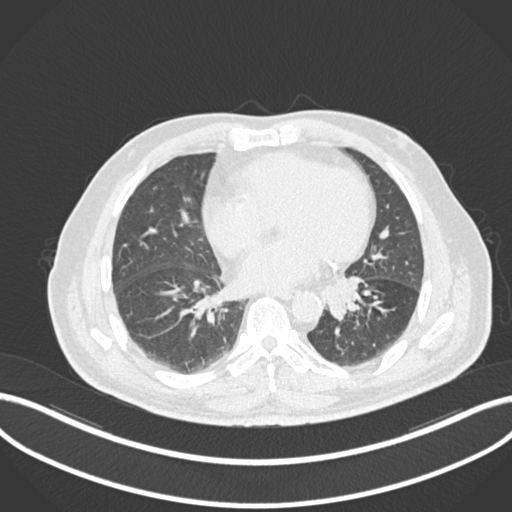
Chest CT, one axial slice; position 46 of 161 along the scan axis; lung window (W 1500 / L -600 HU); 512 × 512 image matrix, field of view 400 × 400 mm. Male patient, age 71 years. Case-level facts recorded for this patient, not image findings: clinical TNM (as recorded): T1b N0 M0.
Structures marked on this image (rectangle marked by the reading radiologist):
- lung tumour (recorded histology: squamous cell carcinoma): bounding box <321,272,366,324> (left, top, right, bottom; pixels)